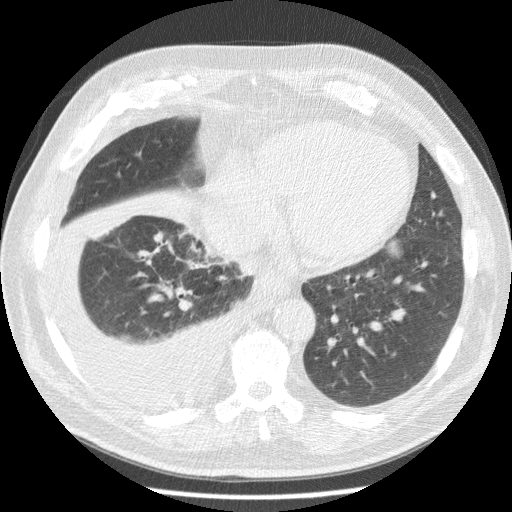
Chest CT (low-dose screening protocol), one axial image, third annual screen, lung window (W 1500 / L -600 HU), 2.5 mm slice thickness, standard (soft-tissue) reconstruction kernel (STANDARD), 512 × 512 image matrix. Male, age 63 years at enrolment. Current smoker at enrolment.
Expert reader's lesion annotation, box from (x=346, y=227) to (x=416, y=302) px. Reader record for this screening exam (exam-level; its link to the box is not recorded): non-calcified nodule or mass ≥4 mm, left lower lobe, 34 × 31 mm, smooth margins, soft tissue attenuation, pre-existing on the prior screen: yes; interval growth: yes. Official screen result: positive, other. Lung cancer was diagnosed 30 days after this screen: squamous cell carcinoma, NOS, left lower lobe, stage IB (AJCC 6th edition), 48 mm at pathology.